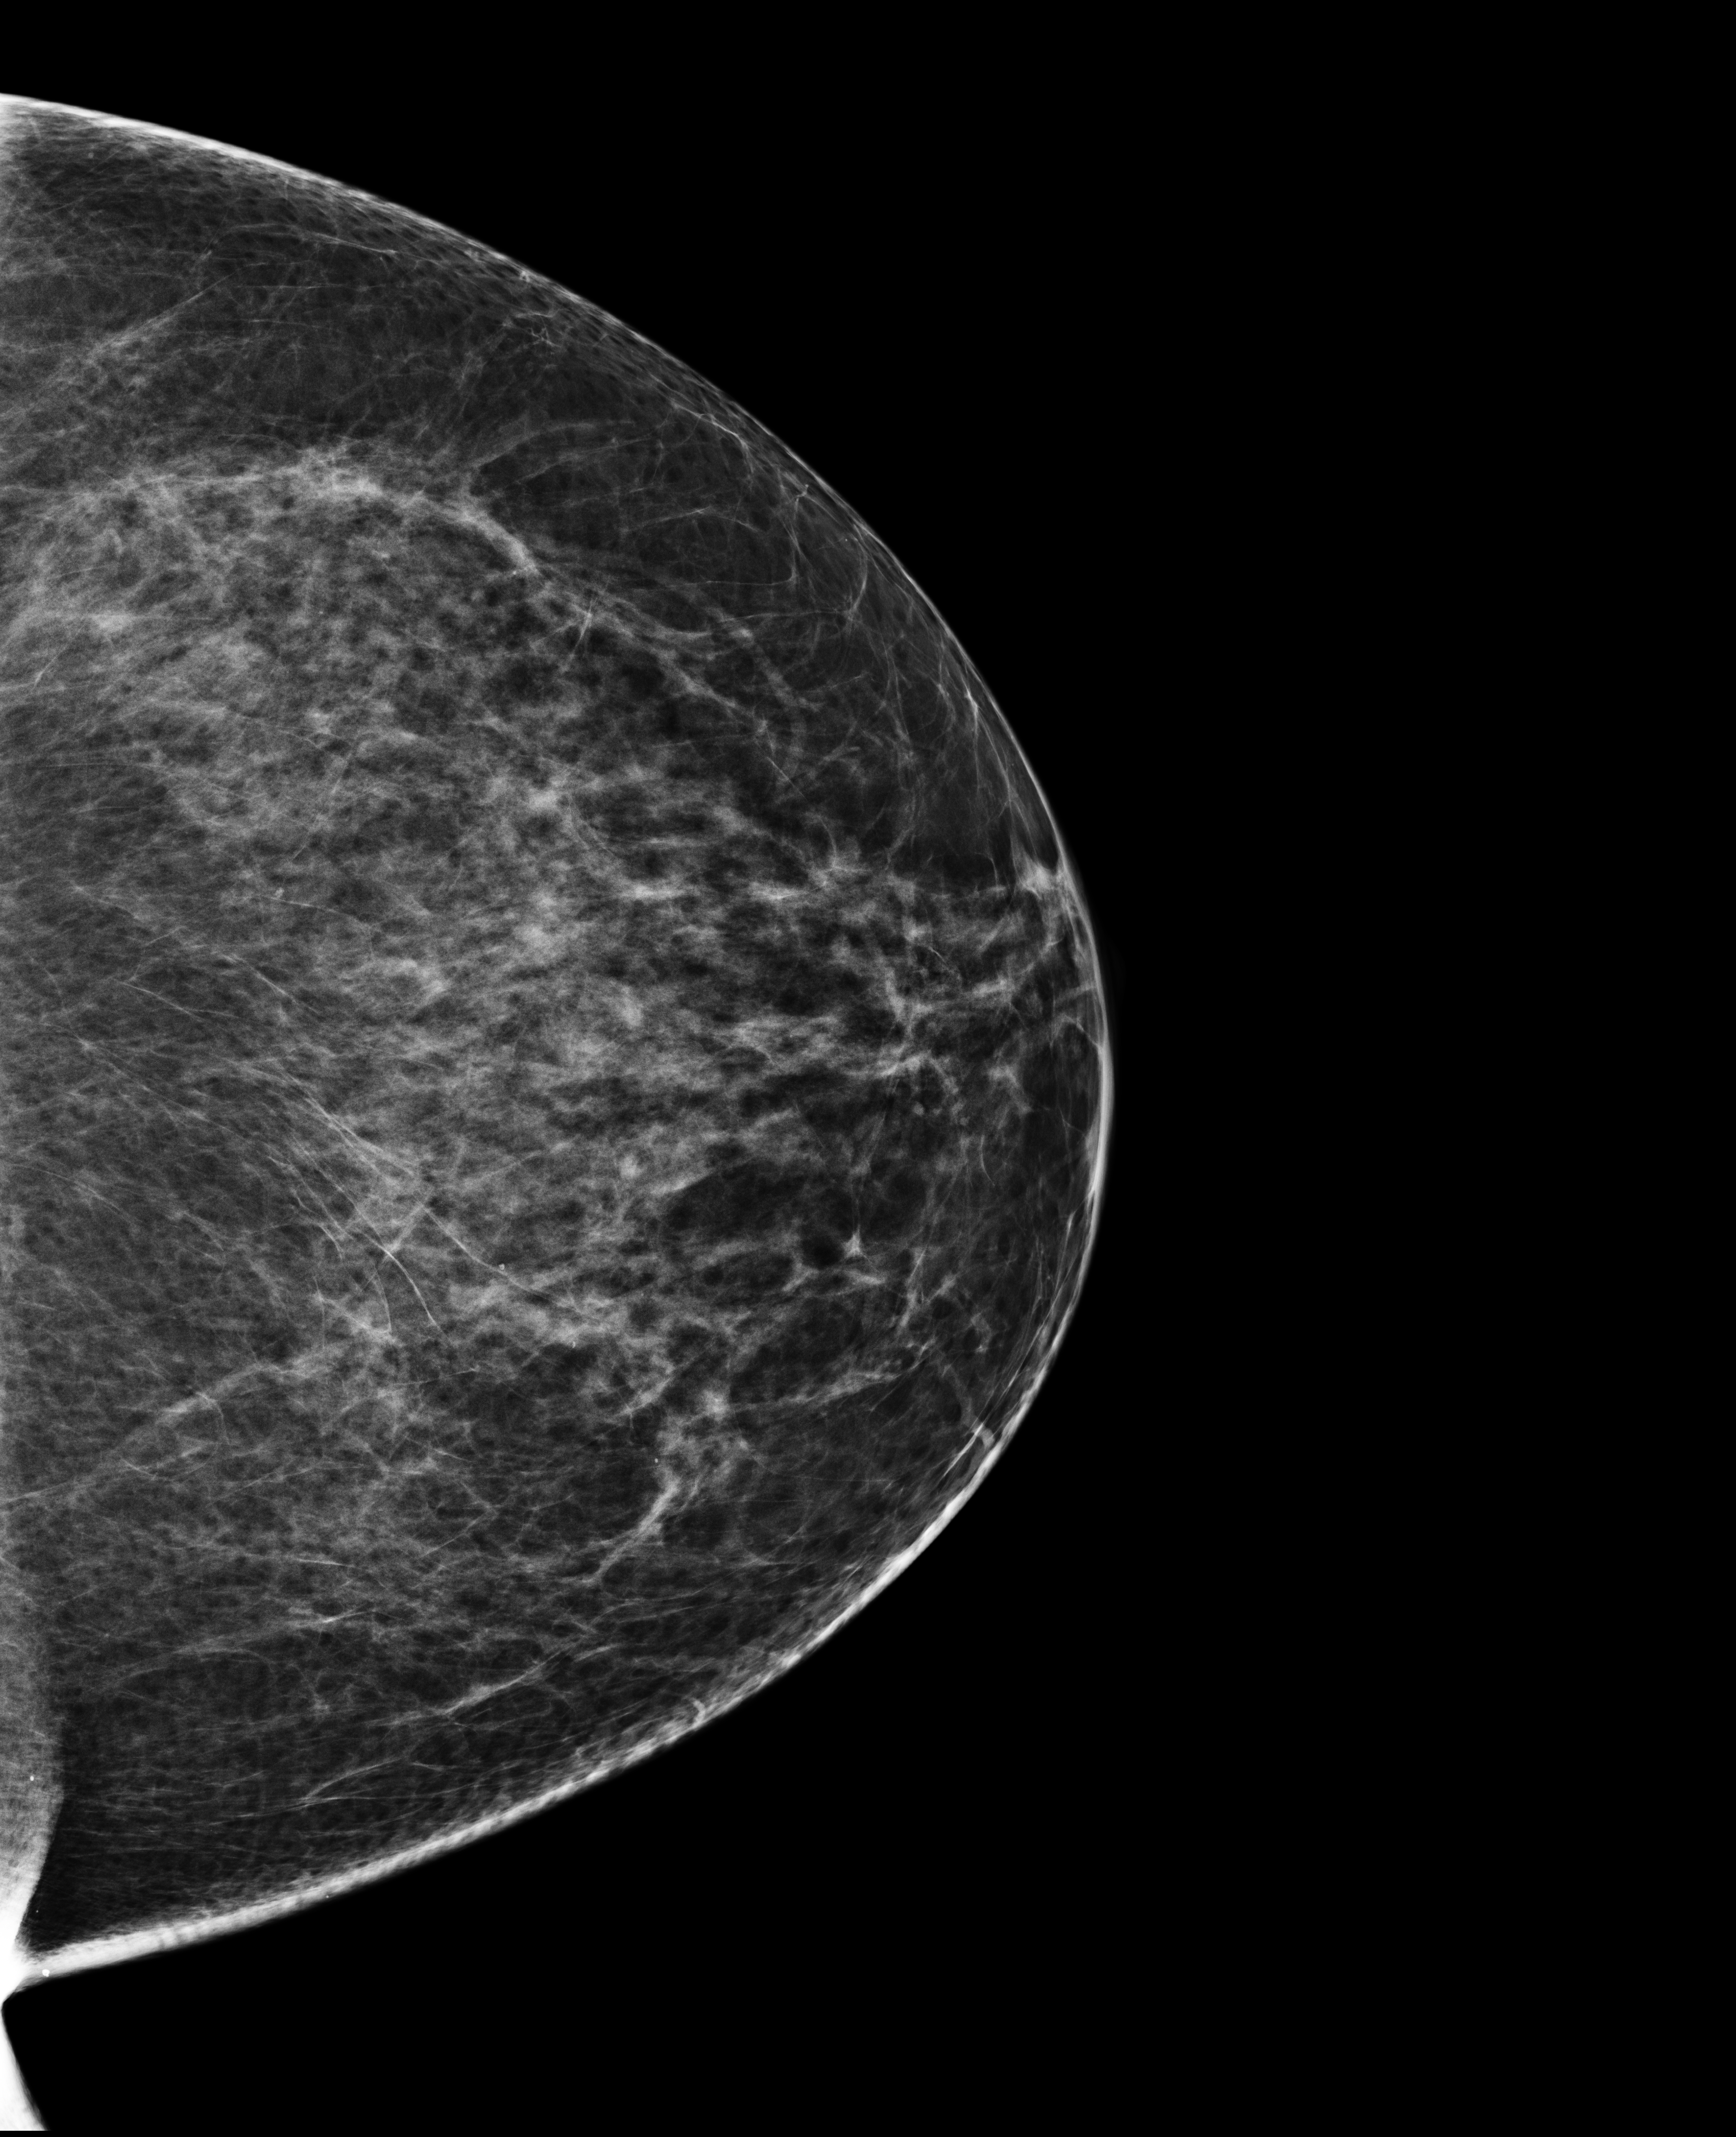
Full-field digital mammogram (FFDM), left breast, craniocaudal (CC) view, diagnostic examination (additional views), compressed breast thickness 83 mm. Patient: female, 56 years.
- breast density at the screening exam (both breasts): heterogeneously dense (BI-RADS density category c)
- final BI-RADS category for the screening round (tomosynthesis exam, both breasts): category 5
- recall: recalled for additional imaging after this screen